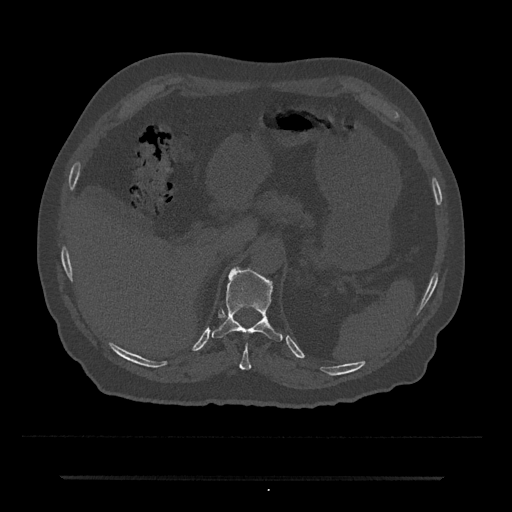
CT including the spine, one axial slice. Position 186 of 797 along the scan axis. Reconstruction kernel Br40s/3. 120 kVp. Bone window (W 1800 / L 400 HU). 0.5 mm slice thickness. 512 × 512 image matrix, field of view 437 × 437 mm. Male patient, age 69 years. From the clinical record (not read from this slice): primary cancer: prostate.
Outlined on this slice (semi-automatic segmentation, software-assisted and operator-edited):
- T10 vertebra: box from (x=239, y=343) to (x=251, y=370) px
- T11 vertebra: (x=212, y=267)–(x=283, y=342)